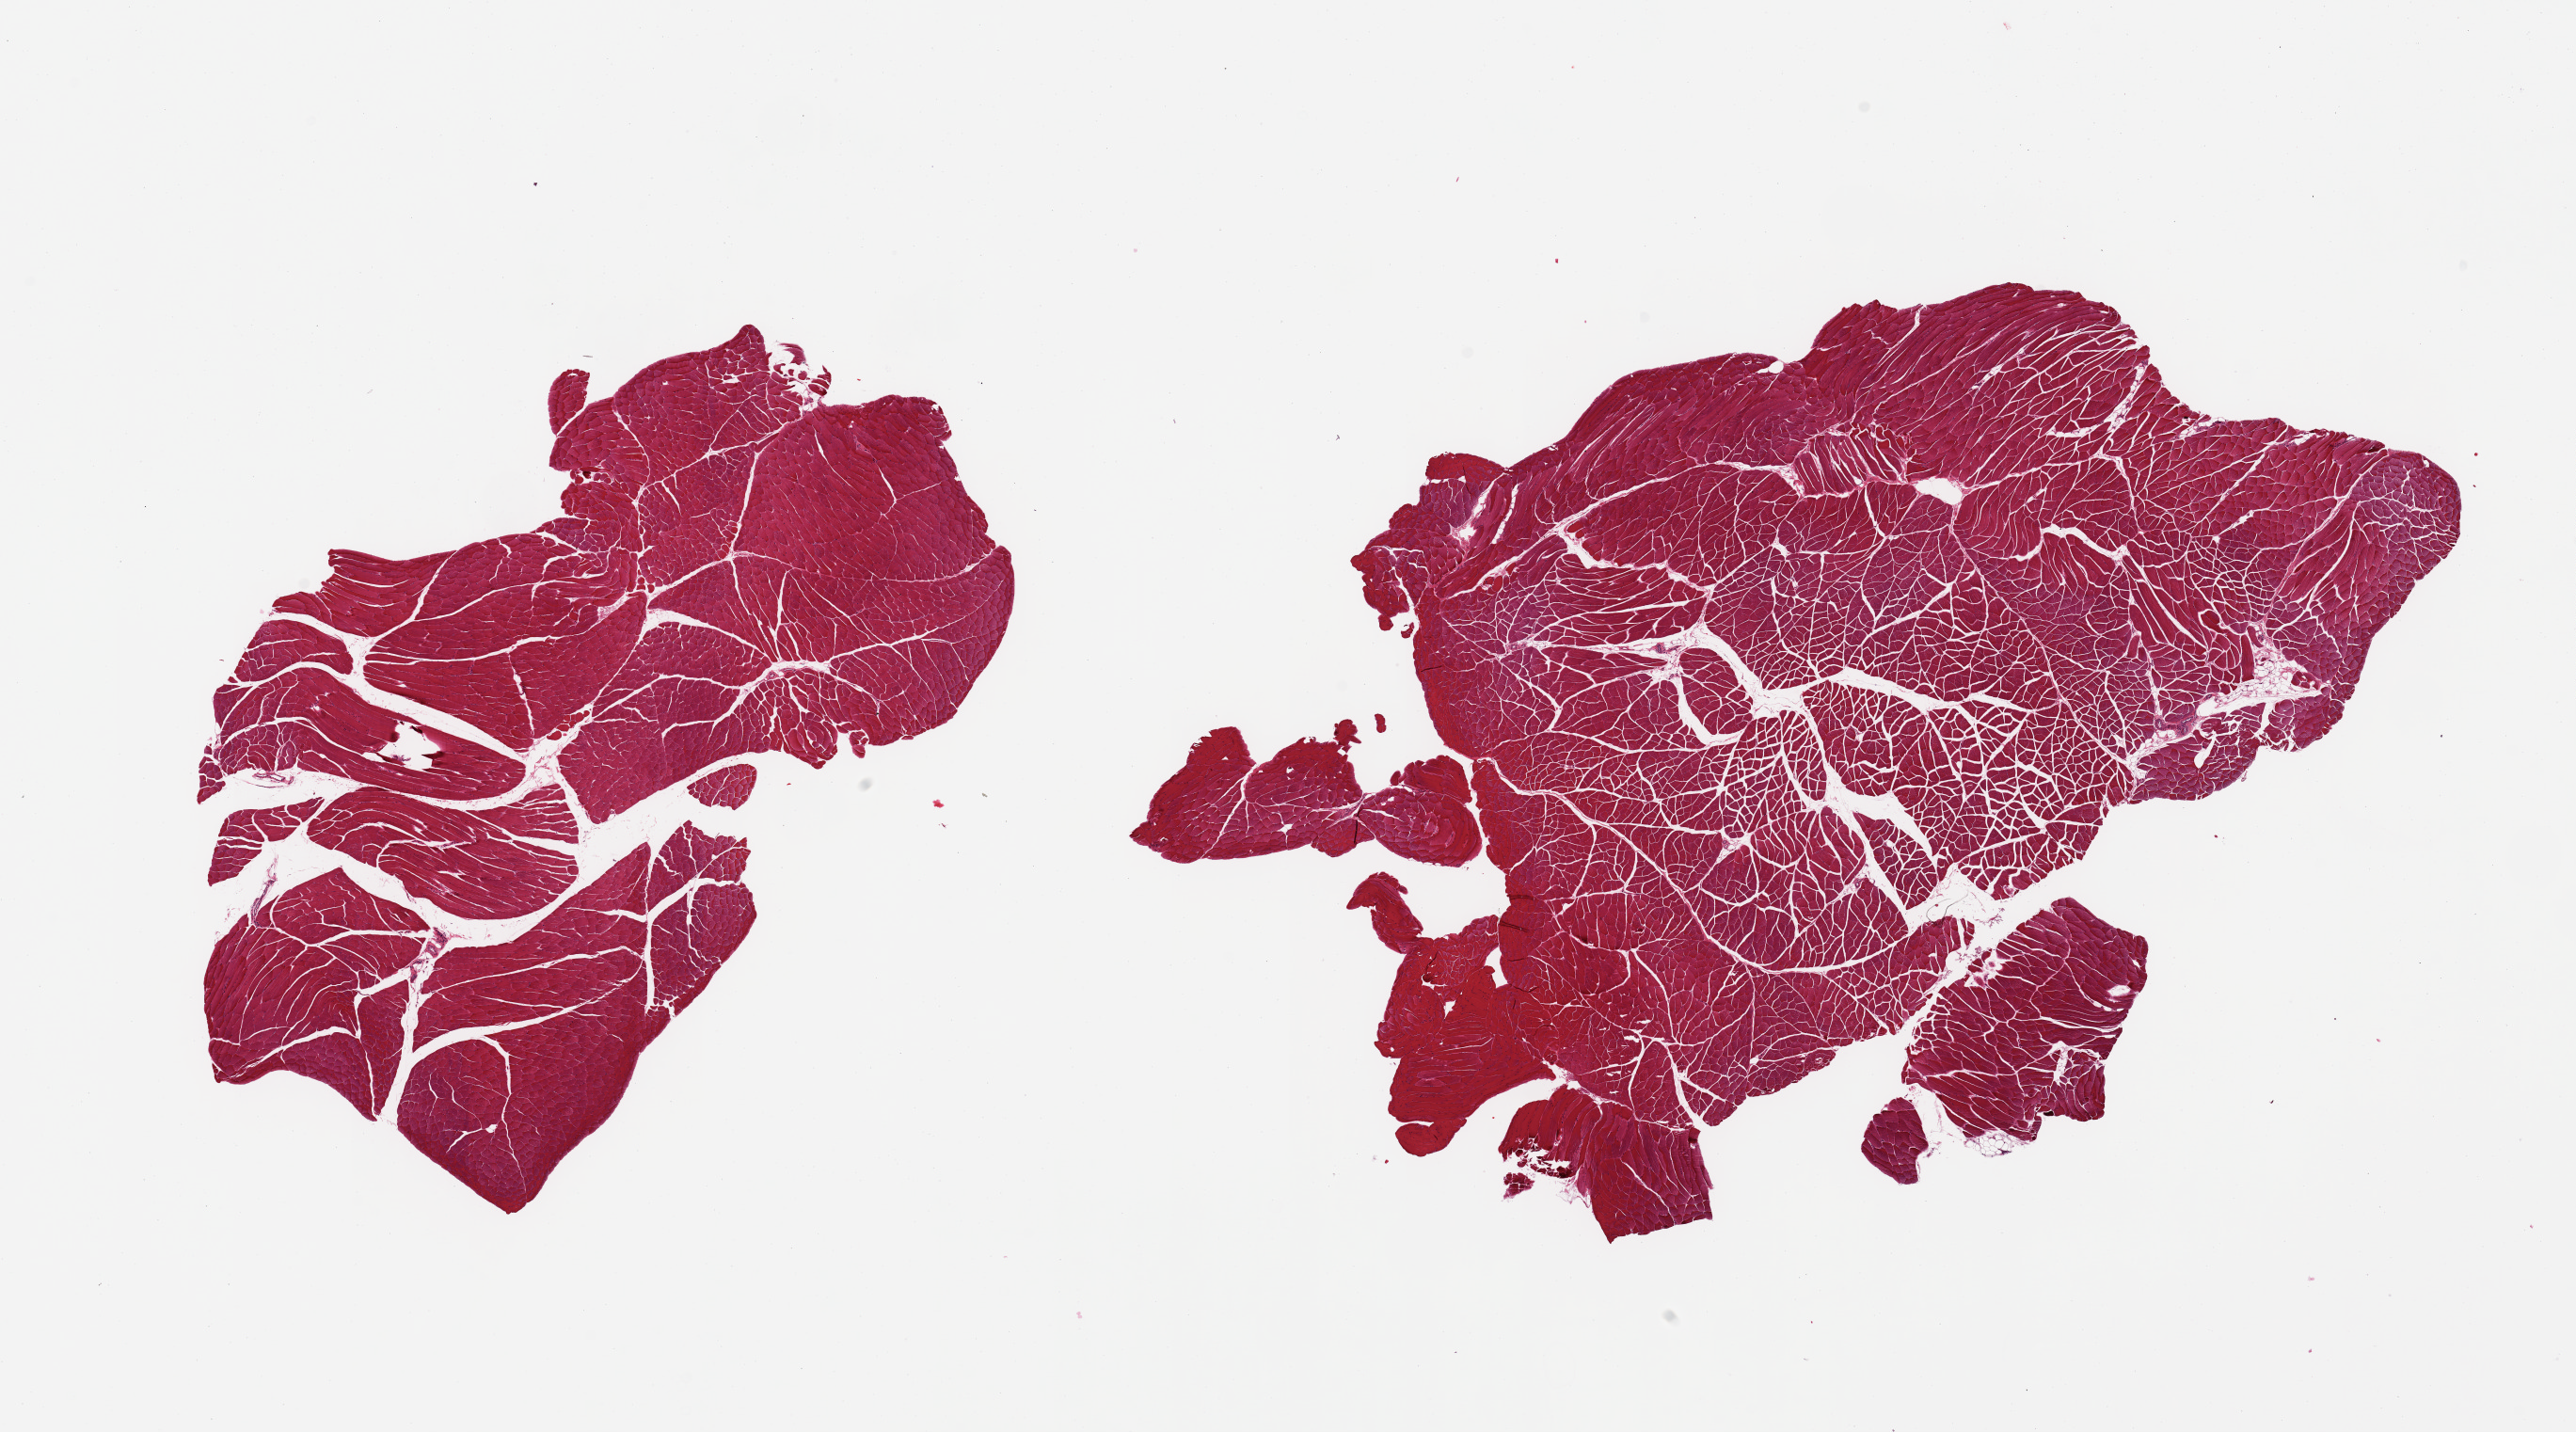
Whole-slide image, H&E stain, brightfield — shown as a low-resolution overview of the whole scanned area (about 21.7 x 12.0 mm), PAXgene-fixed, paraffin-embedded tissue, target tissue: skeletal muscle, tissue donor sample. Donor: female.
Reviewer comment on this tissue sample: 2 pieces, trace interstitial fat.